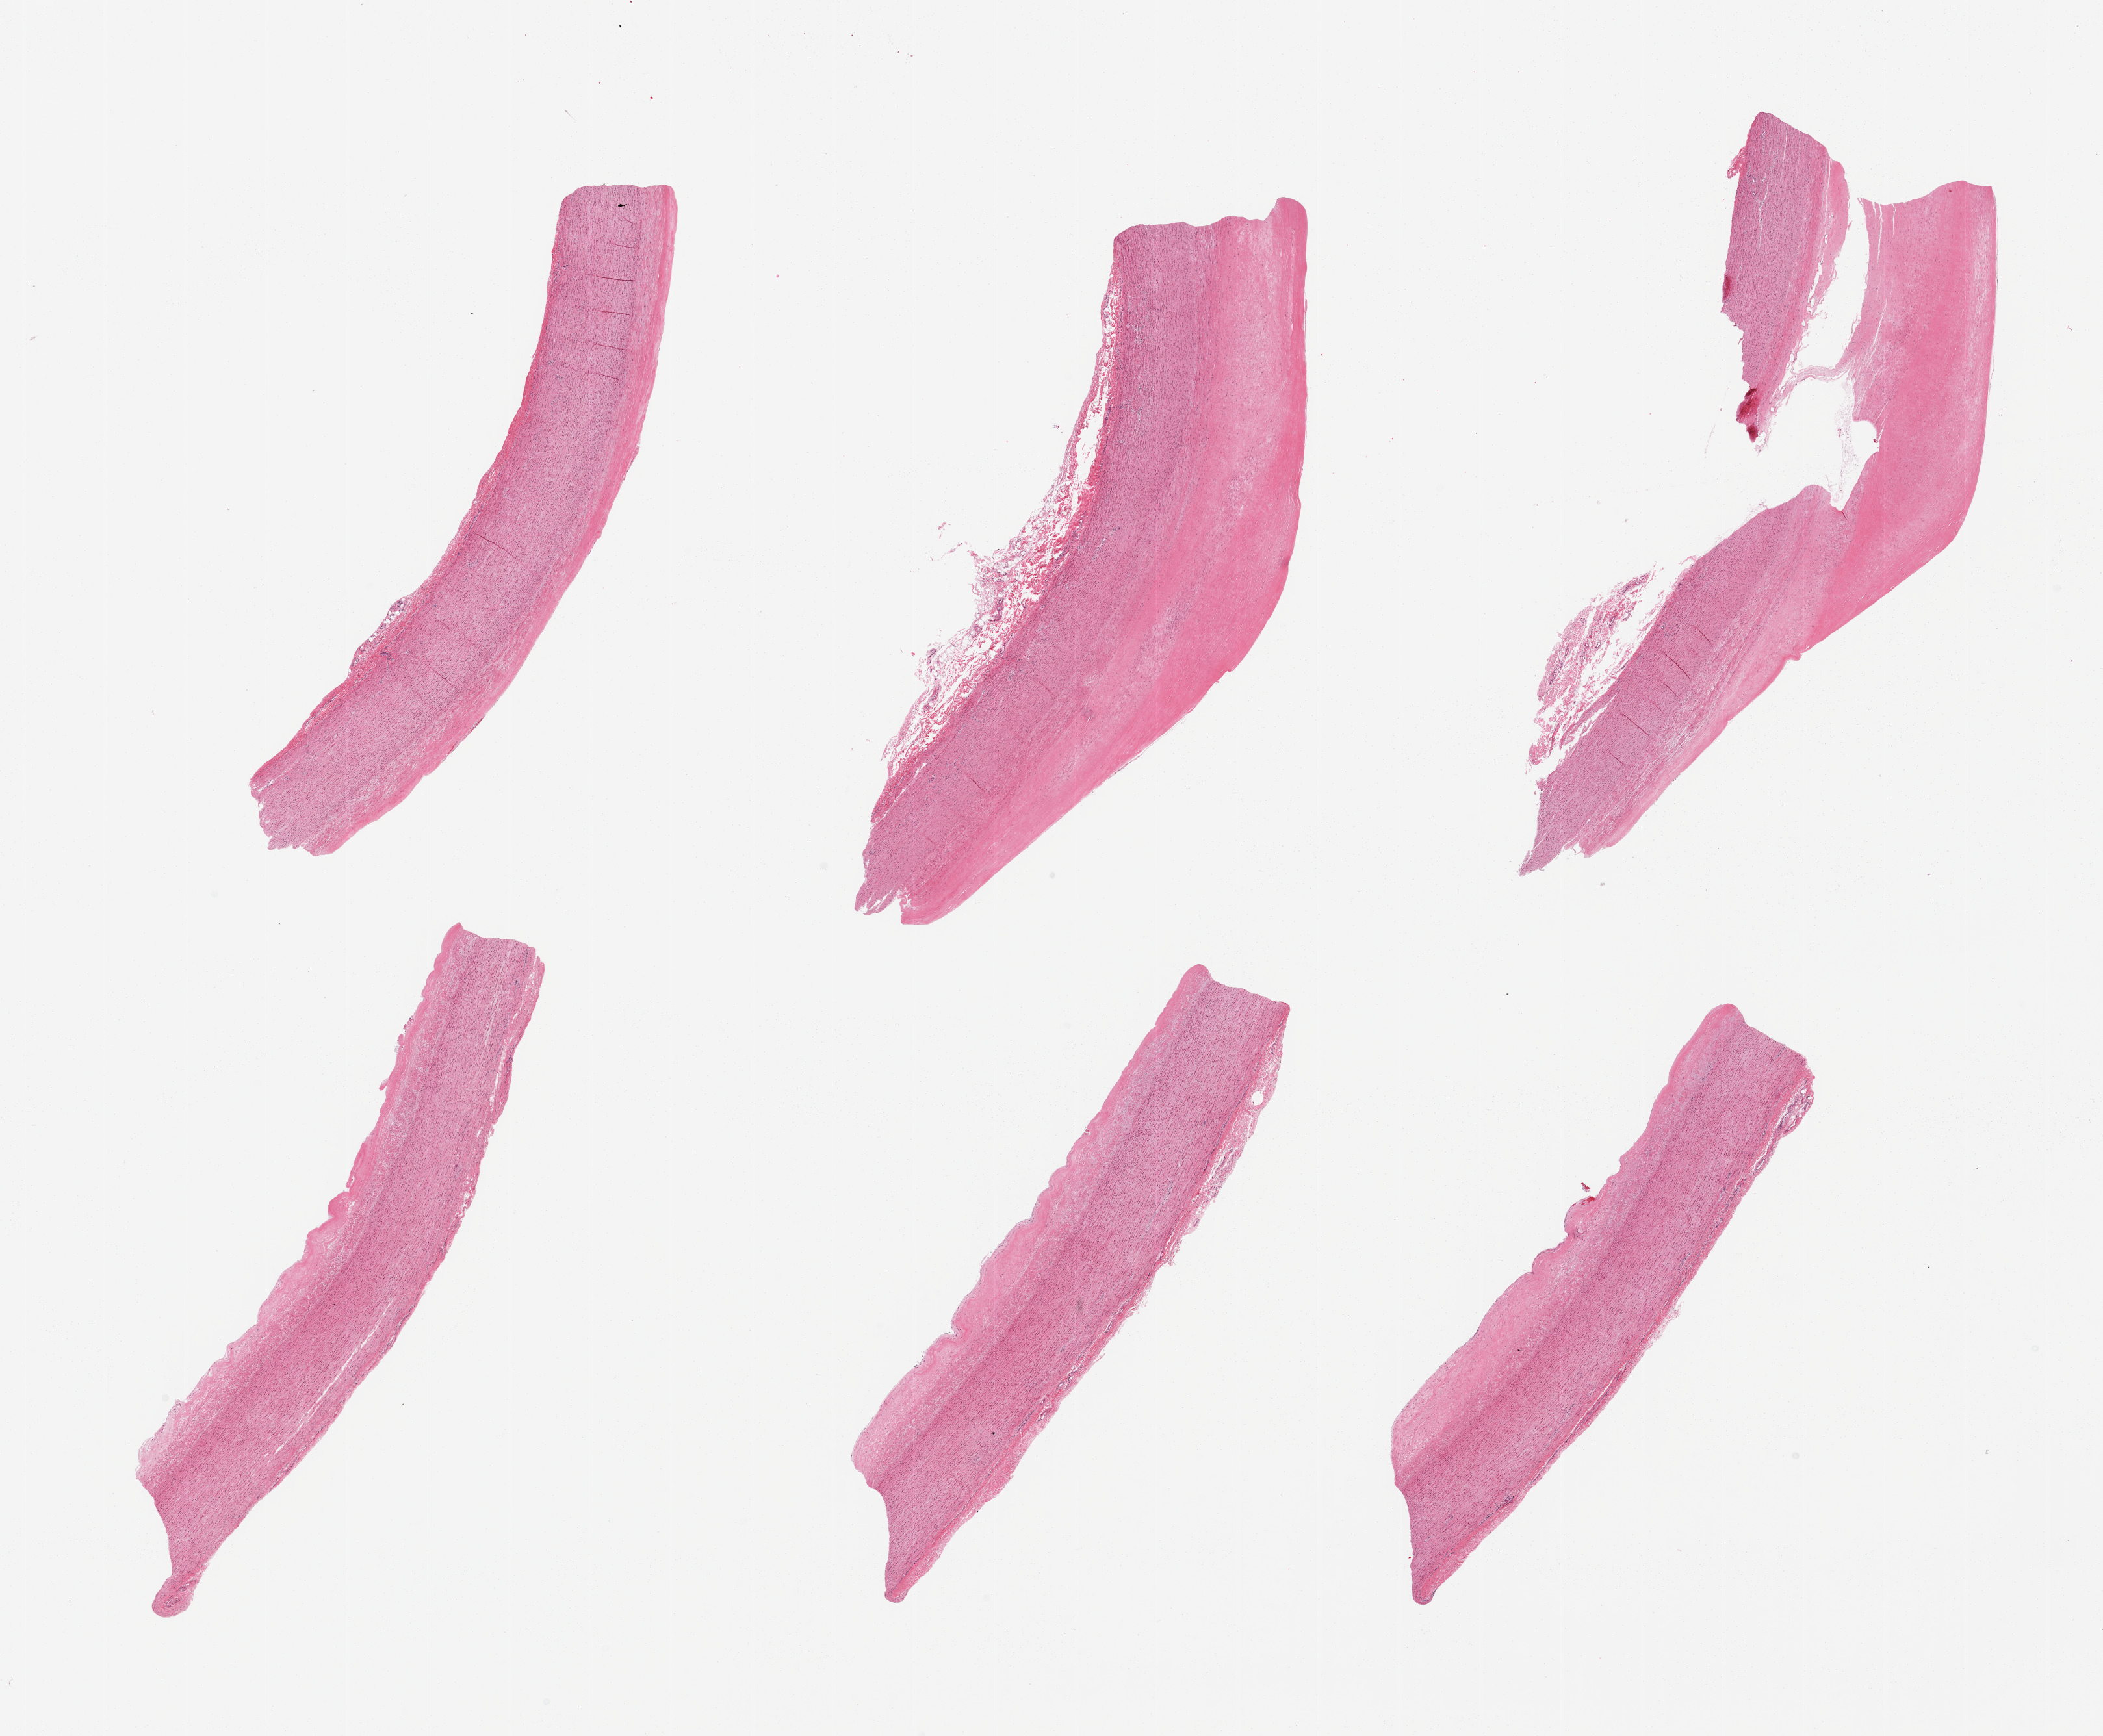
Digitized H&E-stained section, shown as a low-resolution overview of the whole scanned area (about 25.6 x 21.1 mm); PAXgene-fixed, paraffin-embedded tissue; sampled site (target tissue): aorta; donor tissue sample. Female donor.
Review note (as recorded): 6 pieces, 2 have prominent fibroatheromatous plaques.